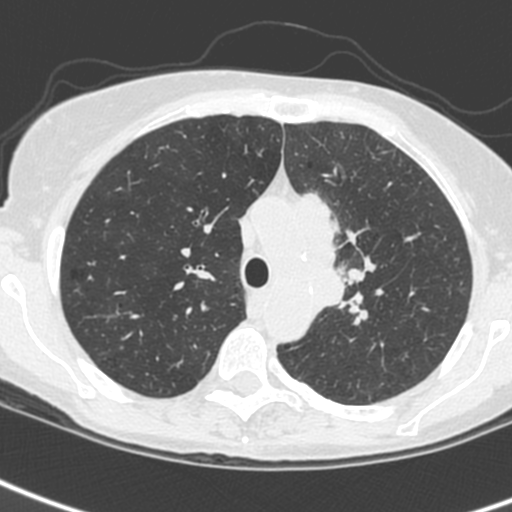
Low-dose screening chest CT, one axial slice; slice 181 of 242 in the series (ordered by position); lung window (W 1500 / L -600 HU); 1.3 mm slice thickness; 512 × 512 image matrix, field of view 284 × 284 mm.
Structures marked on this image (outlined manually by an expert reader):
- lesion 3 (tumor, upper lobe of left lung): bounding box (x1, y1, x2, y2) in pixels: (298, 192, 347, 311)